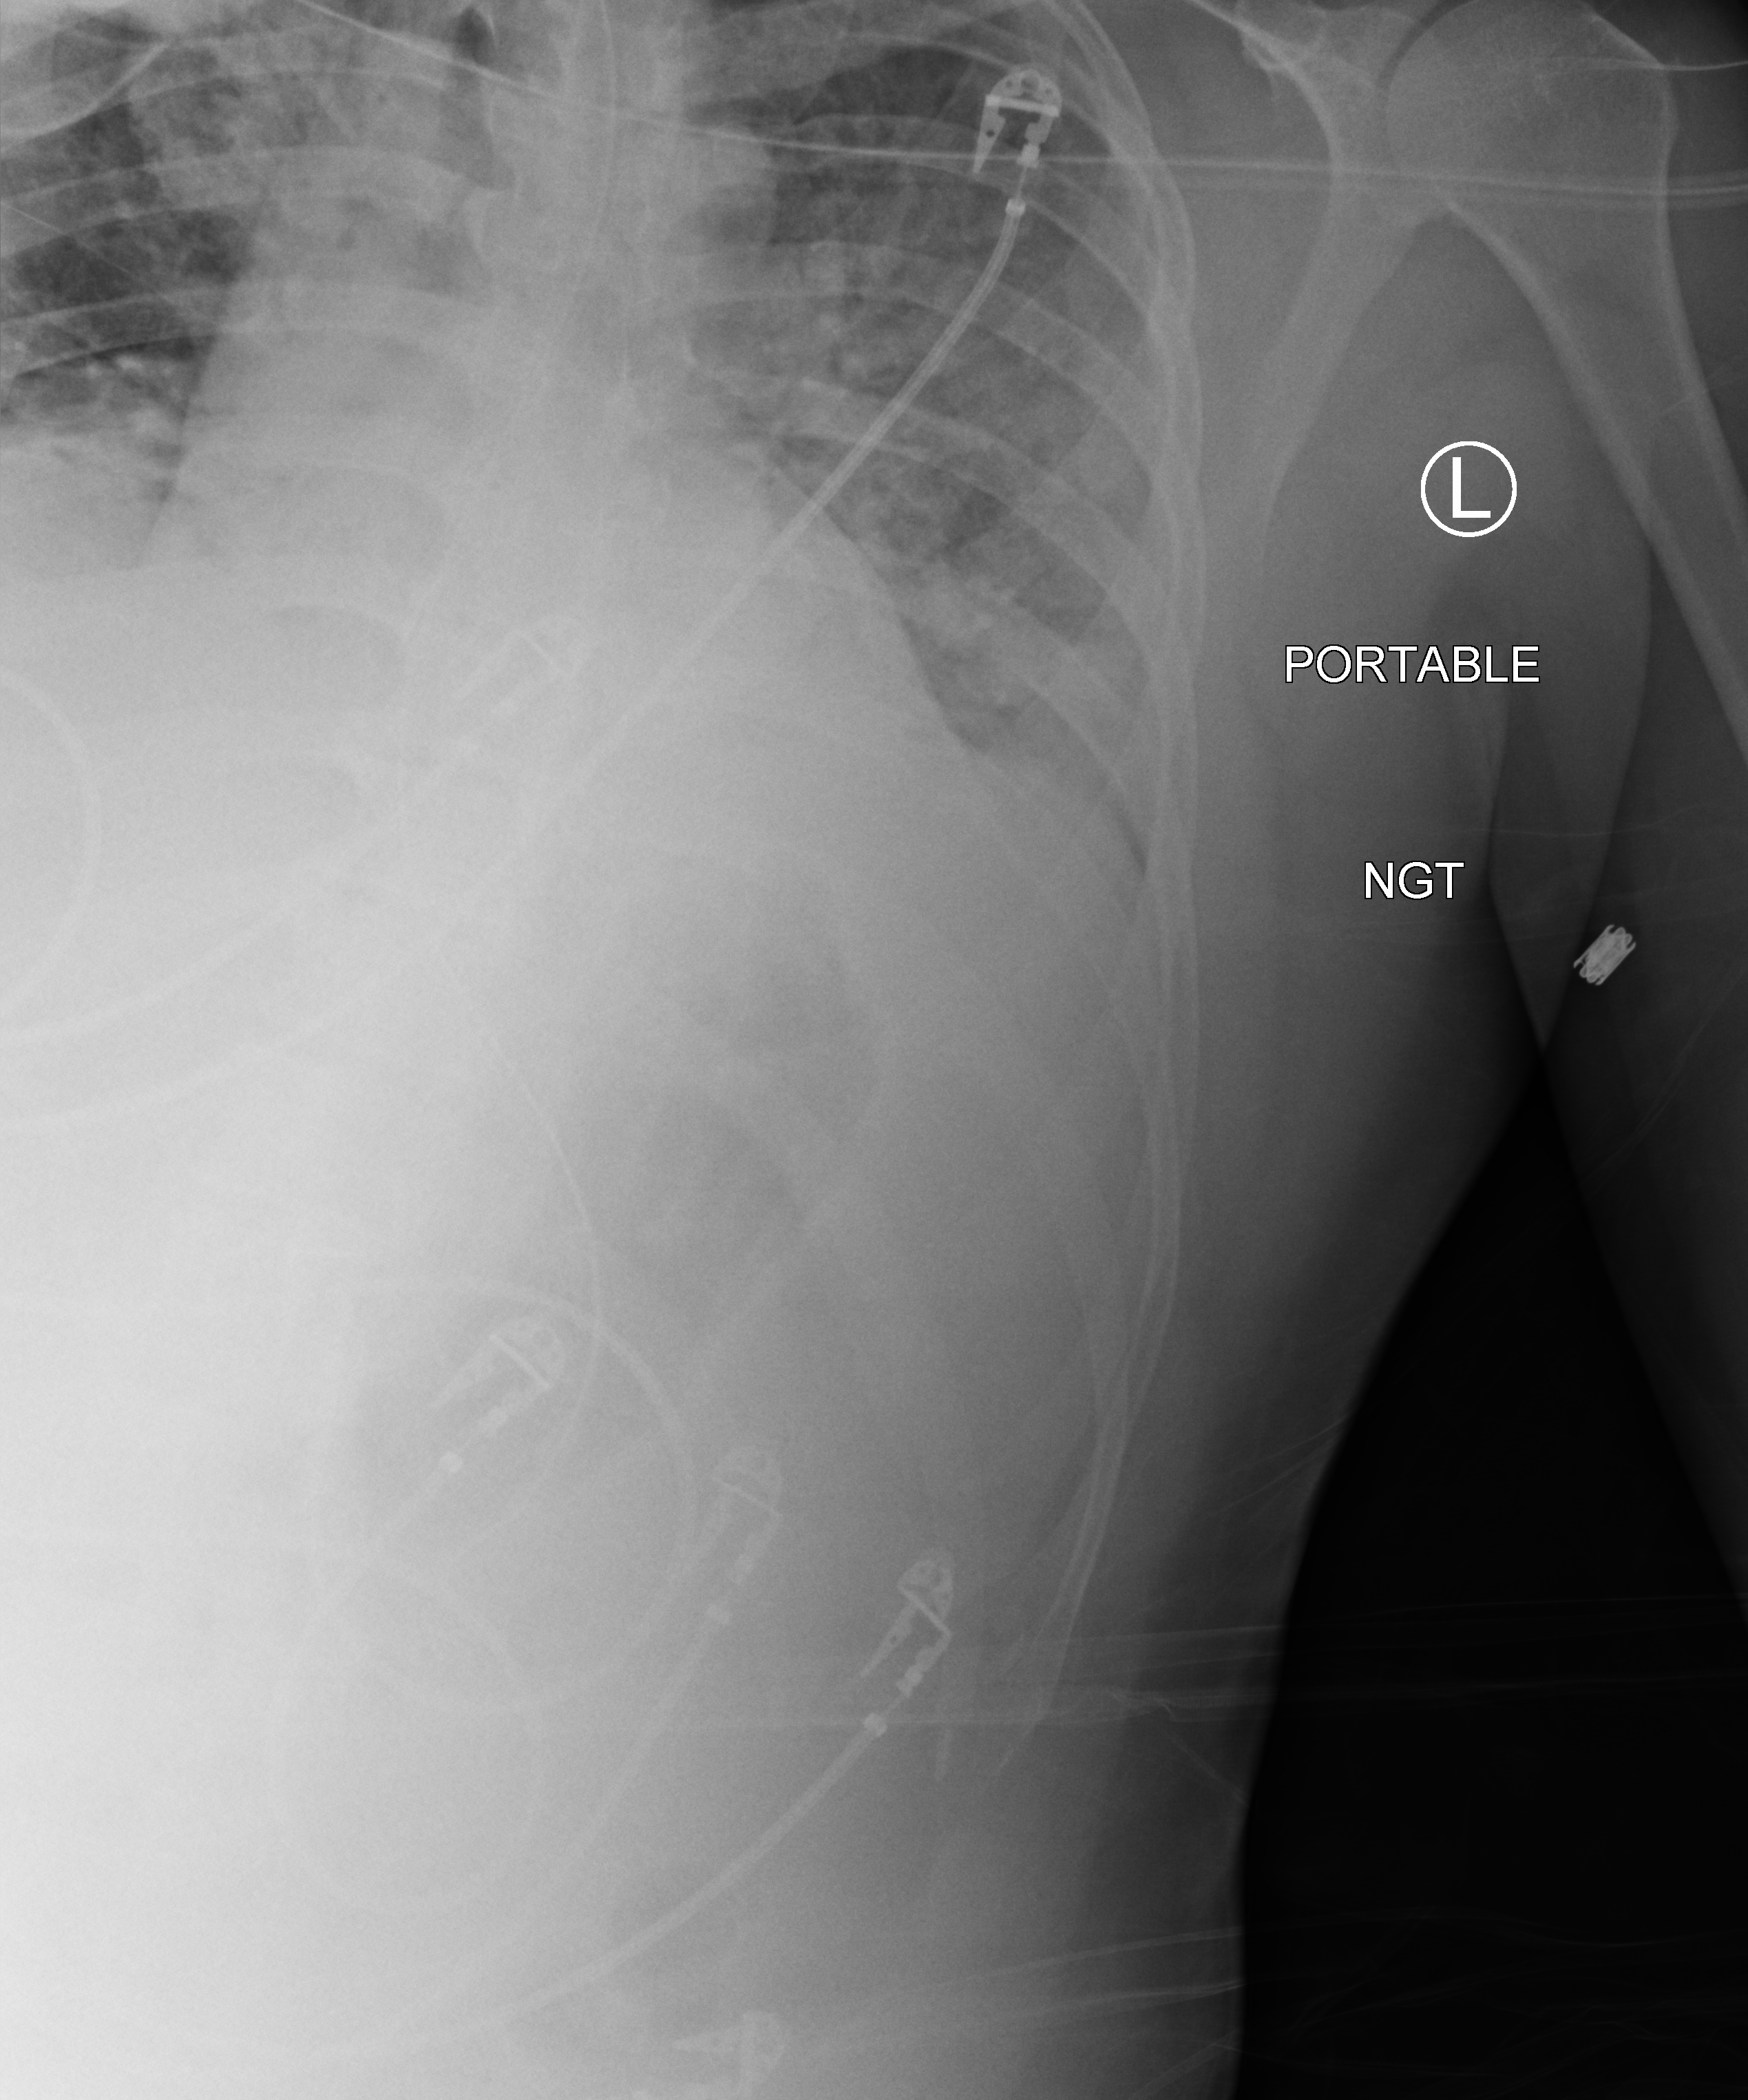
Portable chest radiograph. Male patient hospitalised with COVID-19, age 18–59 years.
Hospital-stay facts (about this admission, not read from this image; timing relative to this image not recorded):
- admitted to intensive care during this hospital stay: yes
- COPD (admission record): no
- length of hospital stay: 18 days